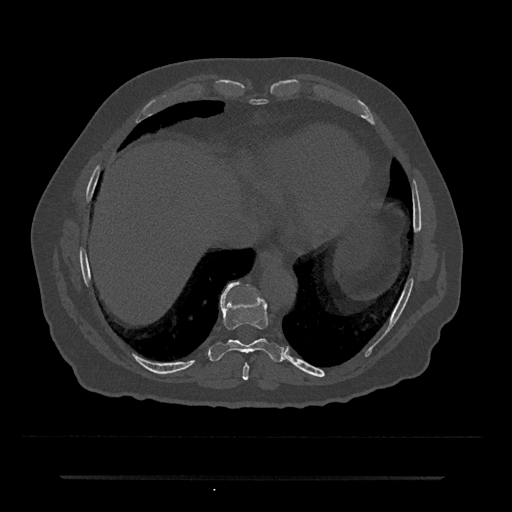
CT including the spine, one axial slice. Slice 278 of 797 in the series (ordered by position). 120 kVp. Bone window (W 1800 / L 400 HU). 512 × 512 image matrix, field of view 437 × 437 mm. Patient: male, 69 years. From the clinical record (not read from this slice): primary cancer: prostate.
Structures marked on this image (semi-automatic segmentation, software-assisted and operator-edited):
- T8 vertebra: bounding box (x1, y1, x2, y2) in pixels: (242, 364, 249, 380)
- T9 vertebra: (210, 282, 285, 362)